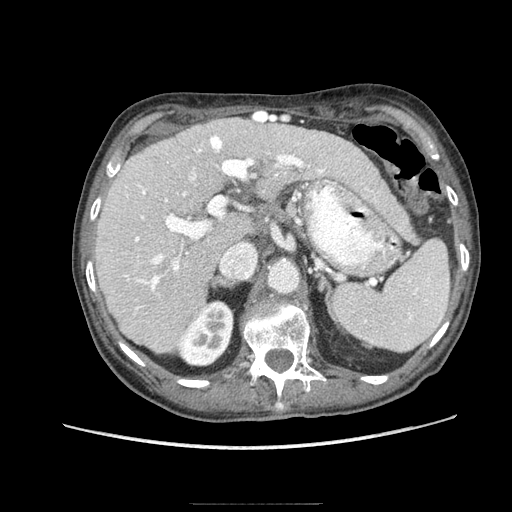
Contrast-enhanced abdominal CT (liver protocol), one axial slice. Position 52 of 83 along the scan axis. Reconstruction kernel STANDARD. 140 kVp. Soft-tissue window (W 400 / L 40 HU). 512 × 512 image matrix, field of view 360 × 360 mm. From the clinical record (not read from this slice): diagnosis: hepatocellular carcinoma (patient treated with transarterial chemoembolisation; whether this scan precedes or follows treatment is not stated here); TNM stage (as recorded): Stage-I; Child-Pugh class: A; tumour differentiation: moderately differentiated; tumour nodularity: uninodular.
Structures marked on this image (semi-automatically segmented with operator editing):
- liver parenchyma outside the tumour (the mass and vessels are separate outlines, so this box may not span the whole liver): bounding box [x1, y1, x2, y2] px = [94, 118, 366, 352]
- liver vessels: [126, 135, 325, 310]